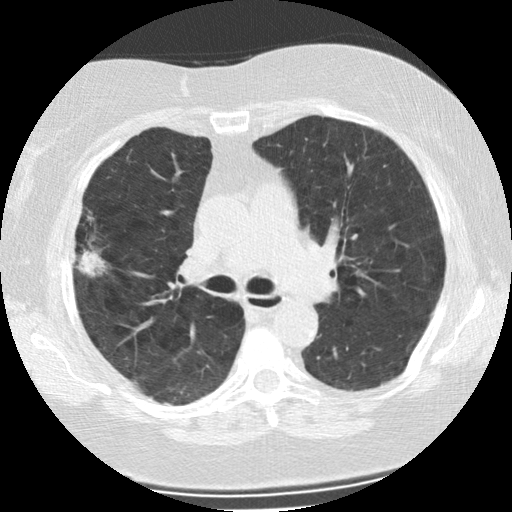
Low-dose screening chest CT, one axial slice; position 144 of 225 along the scan axis; reconstruction kernel STANDARD; lung window (W 1500 / L -600 HU); 2.5 mm slice thickness; 512 × 512 image matrix, field of view 320 × 320 mm.
Structures marked on this image (manually delineated by an expert):
- lesion 1 (tumor, upper lobe of right lung): bounding box [x1, y1, x2, y2] px = [78, 250, 106, 277]